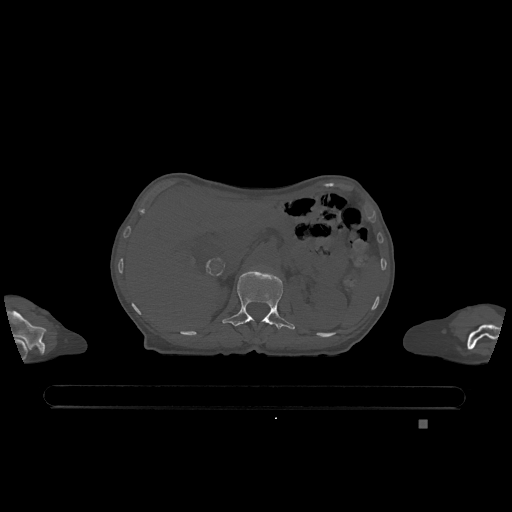
CT including the spine, one axial slice; position 477 of 1317 along the scan axis; bone window (W 1800 / L 400 HU); 0.5 mm slice thickness; 512 × 512 image matrix. Female patient, age 74 years. Case-level facts recorded for this patient, not image findings: primary cancer: lung.
Outlined on this slice (semi-automatically segmented with operator editing):
- L1 vertebra: bounding box <222,270,295,330> (left, top, right, bottom; pixels)